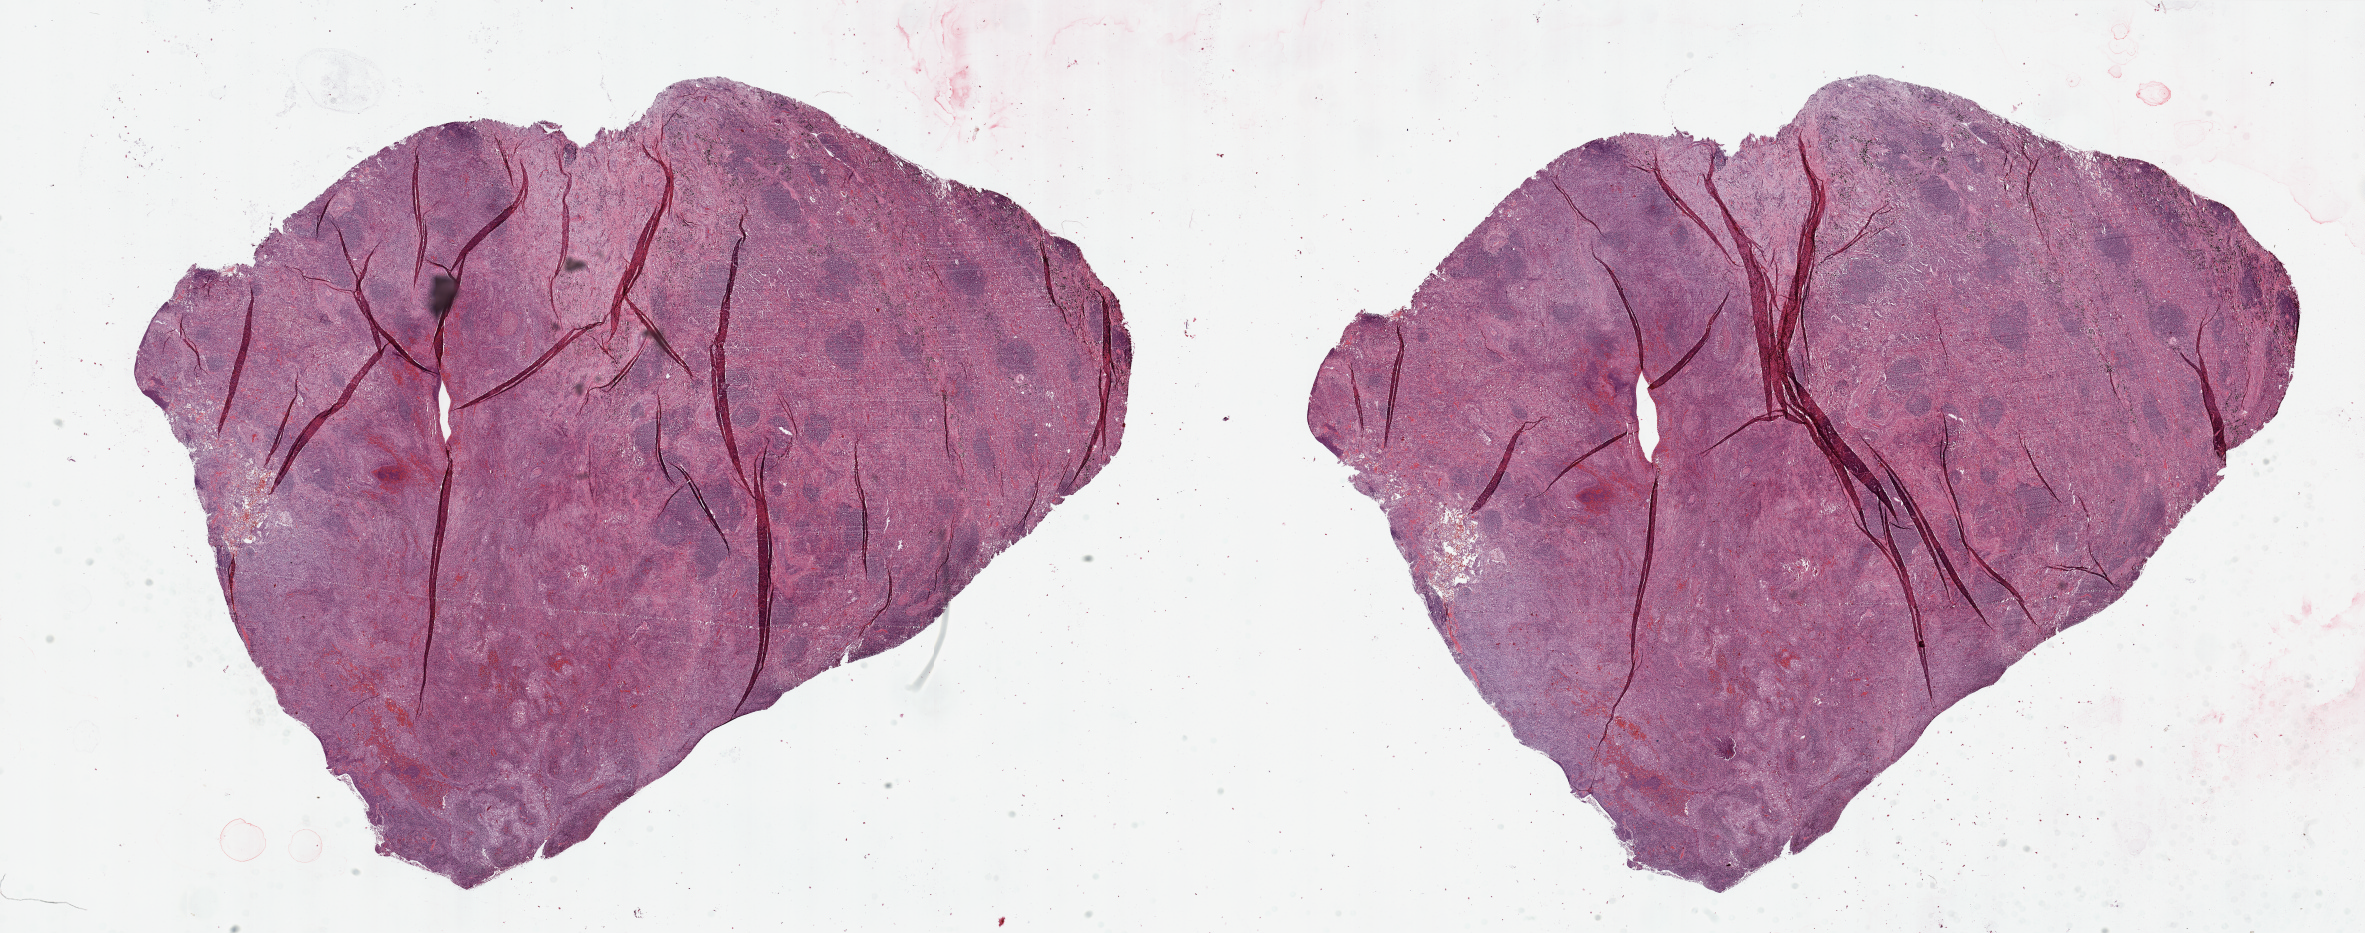
H&E-stained whole-slide image — shown as a low-resolution overview of the whole scanned area (about 37.4 x 14.8 mm). Tumour tissue sample, lung. Patient: male, age 73 years. Histologic grade: G2 (moderately differentiated).
• AJCC pathologic stage: IB
• primary tumour site (as recorded): right lower lobe
• diagnosis: Squamous cell carcinoma, NOS